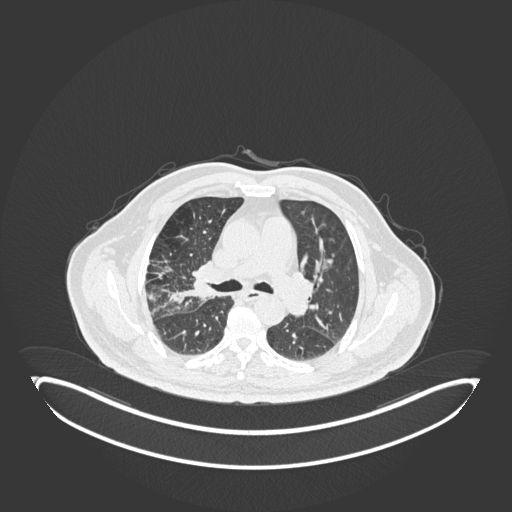
Chest CT, one axial slice; slice 107 of 247 in the series (ordered by position); reconstruction kernel B30f; lung window (W 1500 / L -600 HU); 1 mm slice thickness; 512 × 512 image matrix, field of view 500 × 500 mm. Male patient, age 72 years. Case-level facts recorded for this patient, not image findings: clinical TNM (as recorded): T1c N0 M0; histopathological grade: G2.
Annotated regions visible in this slice (bounding box drawn by a radiologist):
- lung tumour (recorded histology: squamous cell carcinoma): bounding box (x1, y1, x2, y2) in pixels: (169, 264, 214, 311)